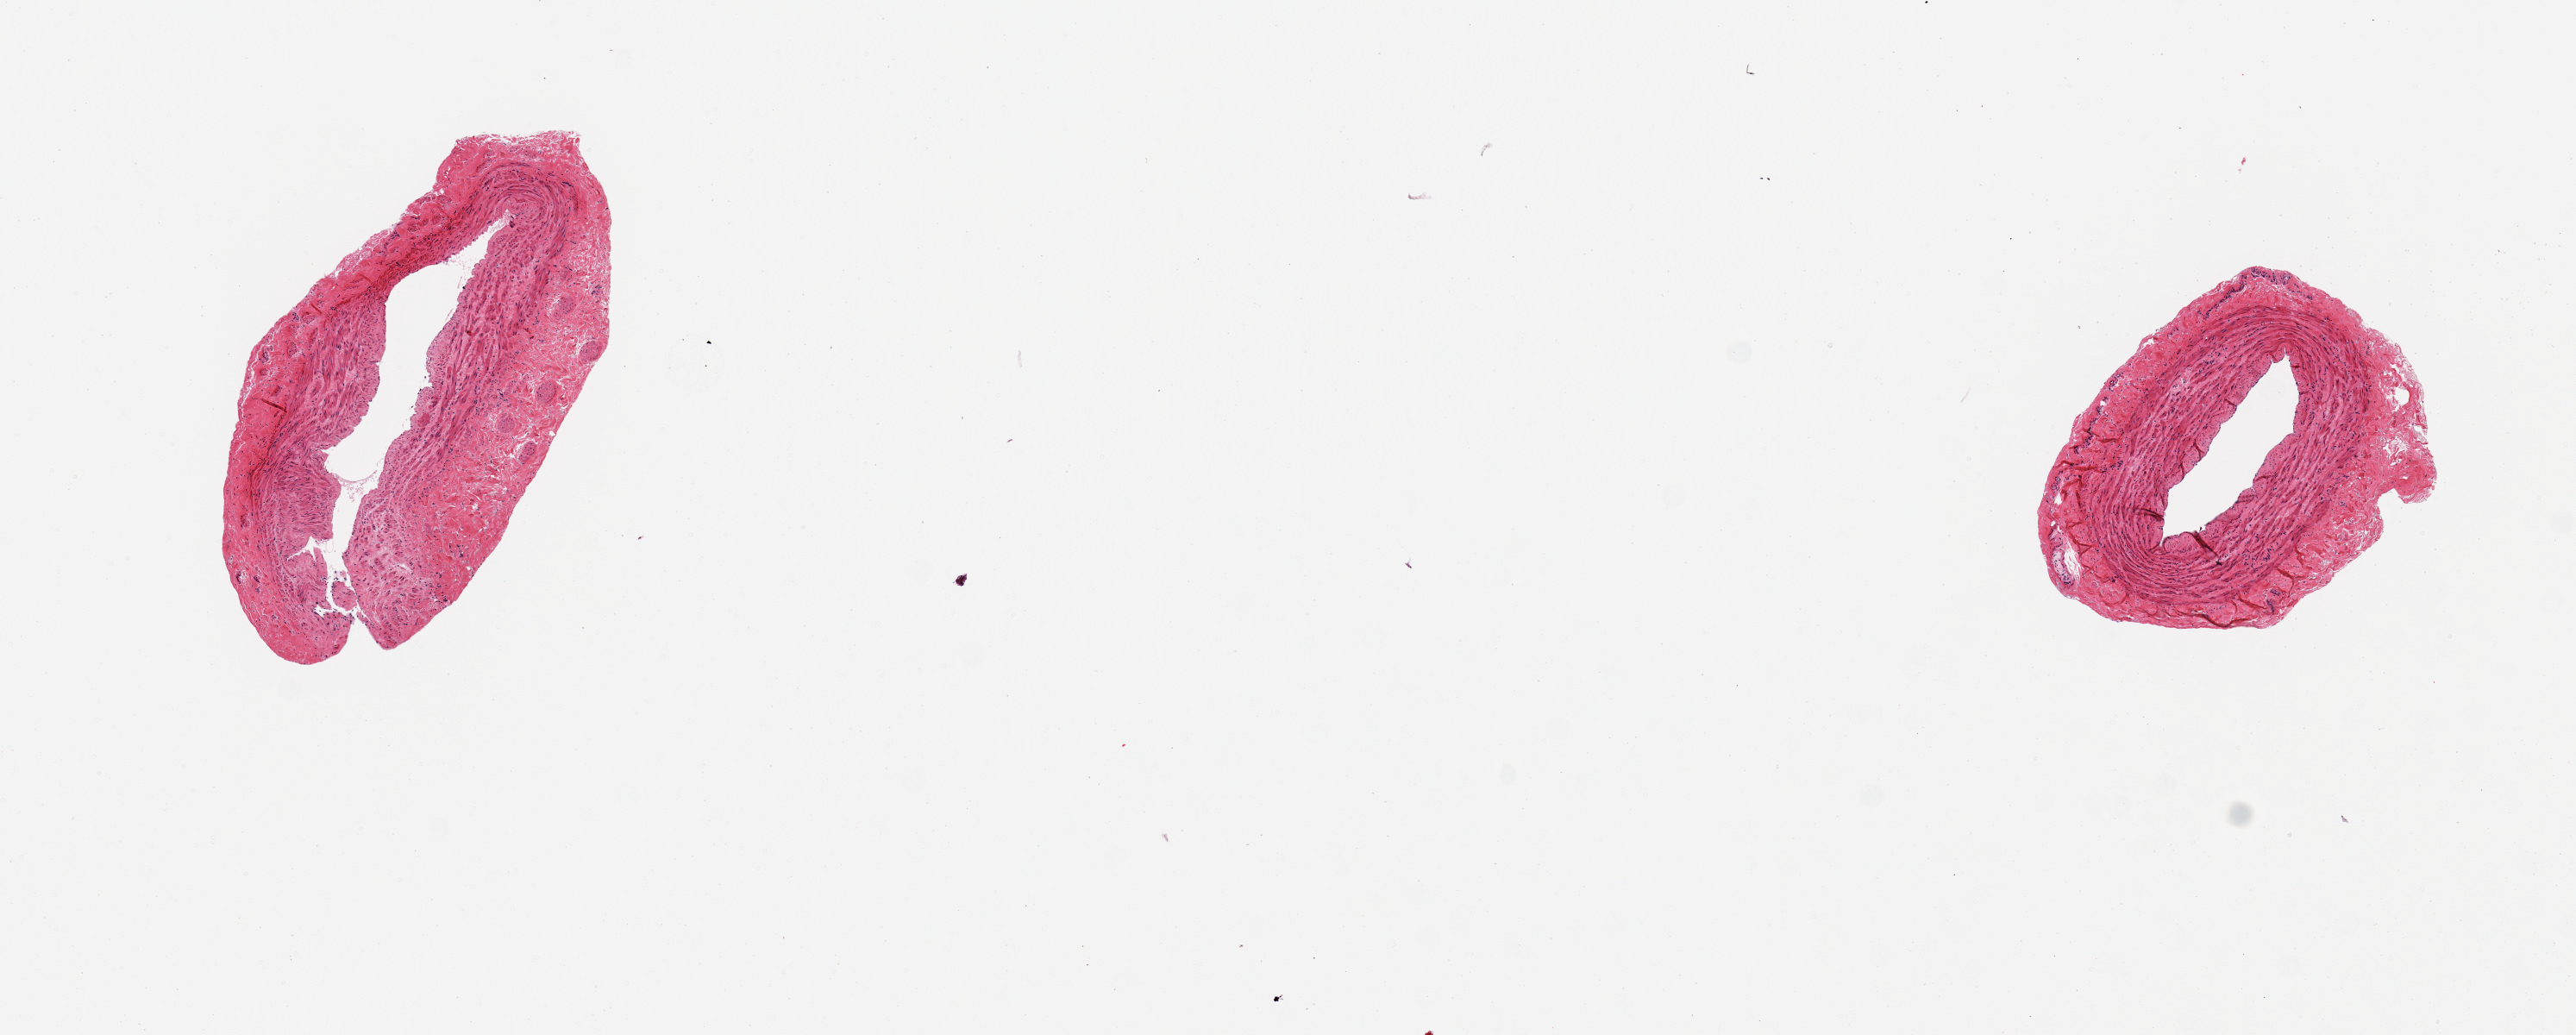
Digitized haematoxylin and eosin-stained section, whole scanned area (about 11.8 x 4.7 mm, slide scanned at 20x) shown as a low-resolution overview; PAXgene-fixed, paraffin-embedded tissue; section of tibial artery (target tissue); donor tissue sample. Donor sex: male.
Review note (as recorded): 2 pieces; no adherent fat.